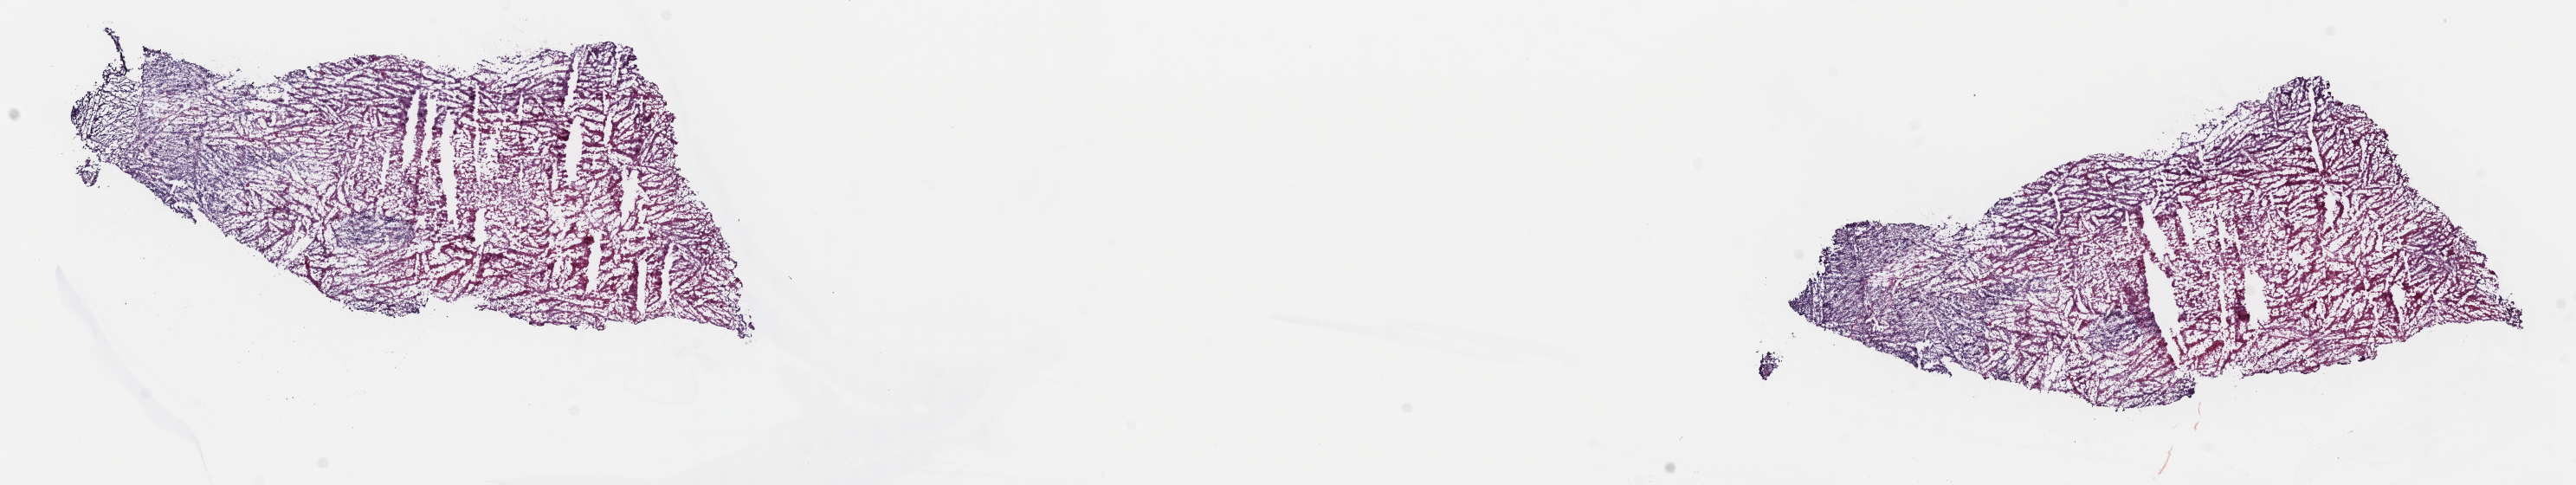
Digitized H&E tissue section (whole slide) — shown as a low-resolution overview of the whole scanned area (about 23.5 x 4.4 mm, acquisition: 40x scan). Frozen section. Sample: primary tumour, uterus. Patient sex: female. Composition of this section per pathologist review: tumour cells 70%, tumour nuclei 70%, normal cells 0%, stromal cells 10%, necrosis 20%. Infiltration values recorded for this section: lymphocyte infiltration 40%, monocyte infiltration 20%, neutrophil infiltration 20%.
Diagnosis: Carcinosarcoma, NOS (endometrium). FIGO stage: IIIC1.